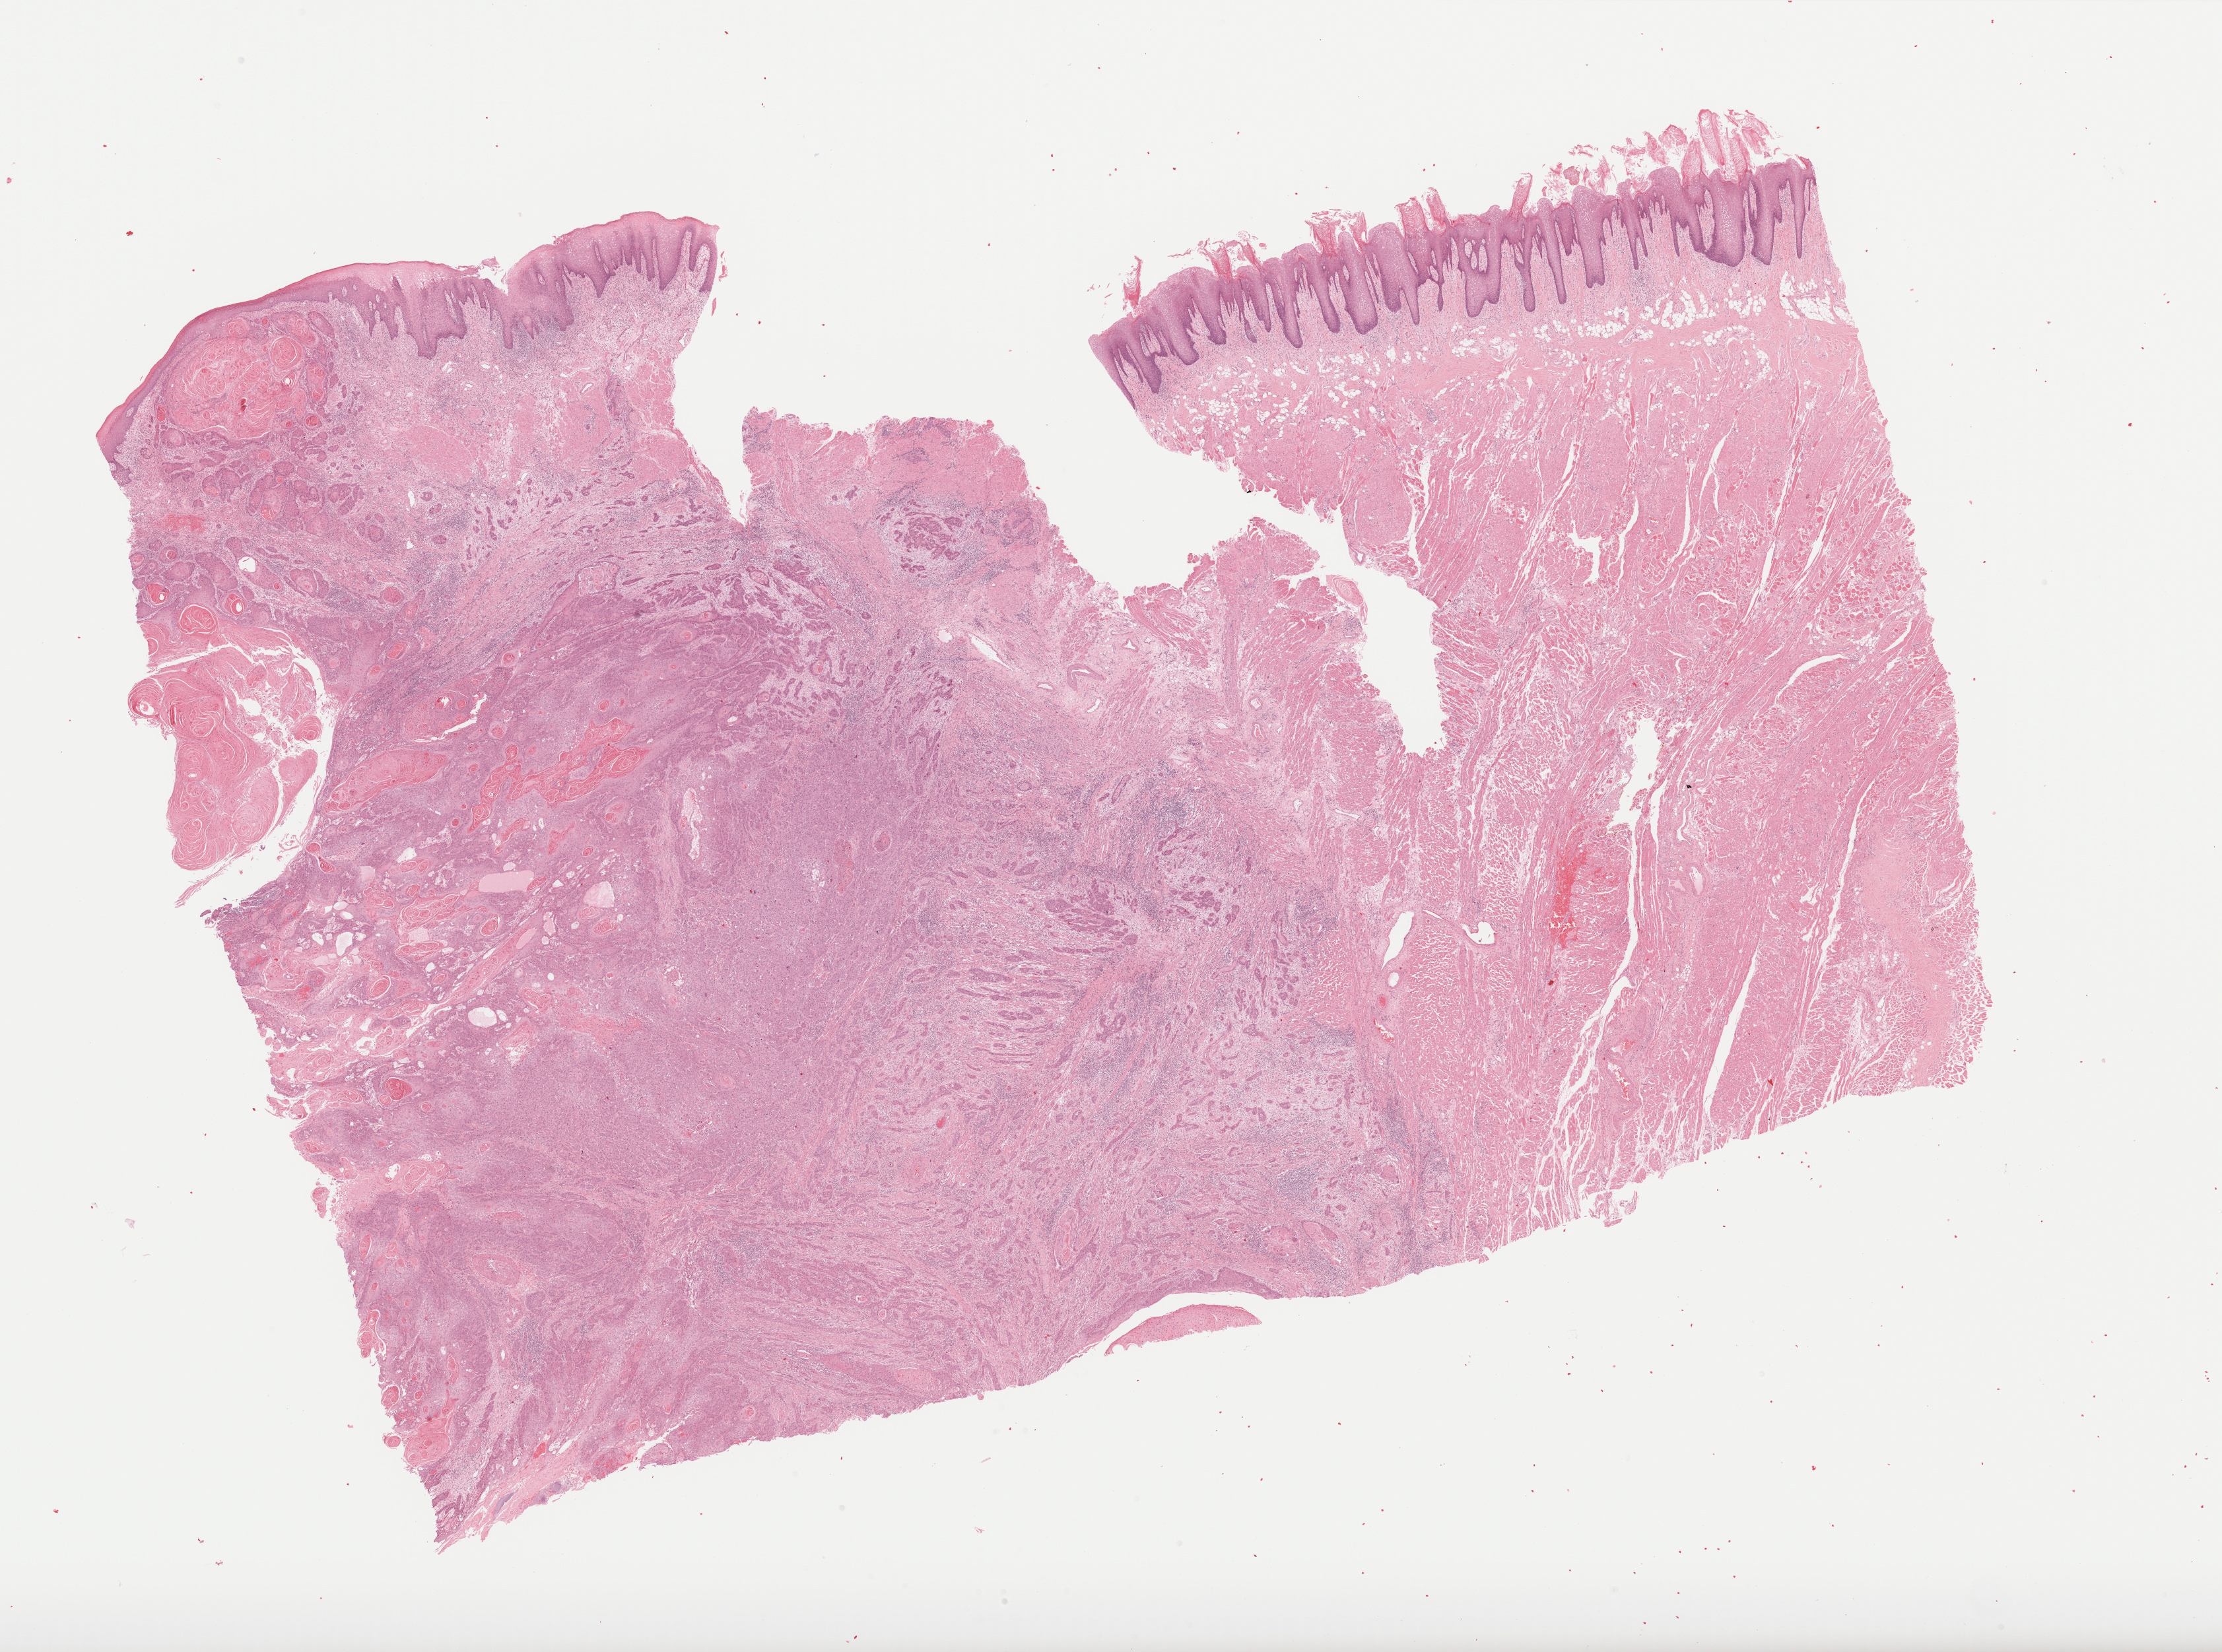
H&E whole-slide image, shown as a low-resolution overview of the whole scanned area (about 27.1 x 20.2 mm, slide scanned at 40x), formalin-fixed paraffin-embedded (FFPE) diagnostic section, sample: primary tumour, head and neck. Patient: male, age at initial diagnosis 77 years. Histologic grade: G2 (moderately differentiated).
AJCC pathologic stage: IVA (6th edition). TNM: T3 N2c. Diagnosis: Squamous cell carcinoma, NOS (overlapping lesion of lip, oral cavity and pharynx).